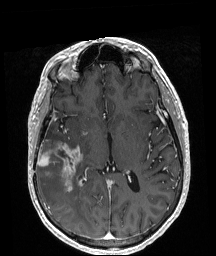
Brain MRI from a brain-tumour surgery series, one axial slice; slice 104 of 208 in the series (ordered by position); T1-weighted post-contrast; 1 mm slice thickness; 216 × 256 image matrix. Case-level facts recorded for this patient, not image findings: histopathology: Astrocytoma; WHO grade: 4; IDH mutation: yes.
Structures marked on this image (manually delineated by an expert):
- tumour: bounding box [x1, y1, x2, y2] px = [38, 143, 81, 192]